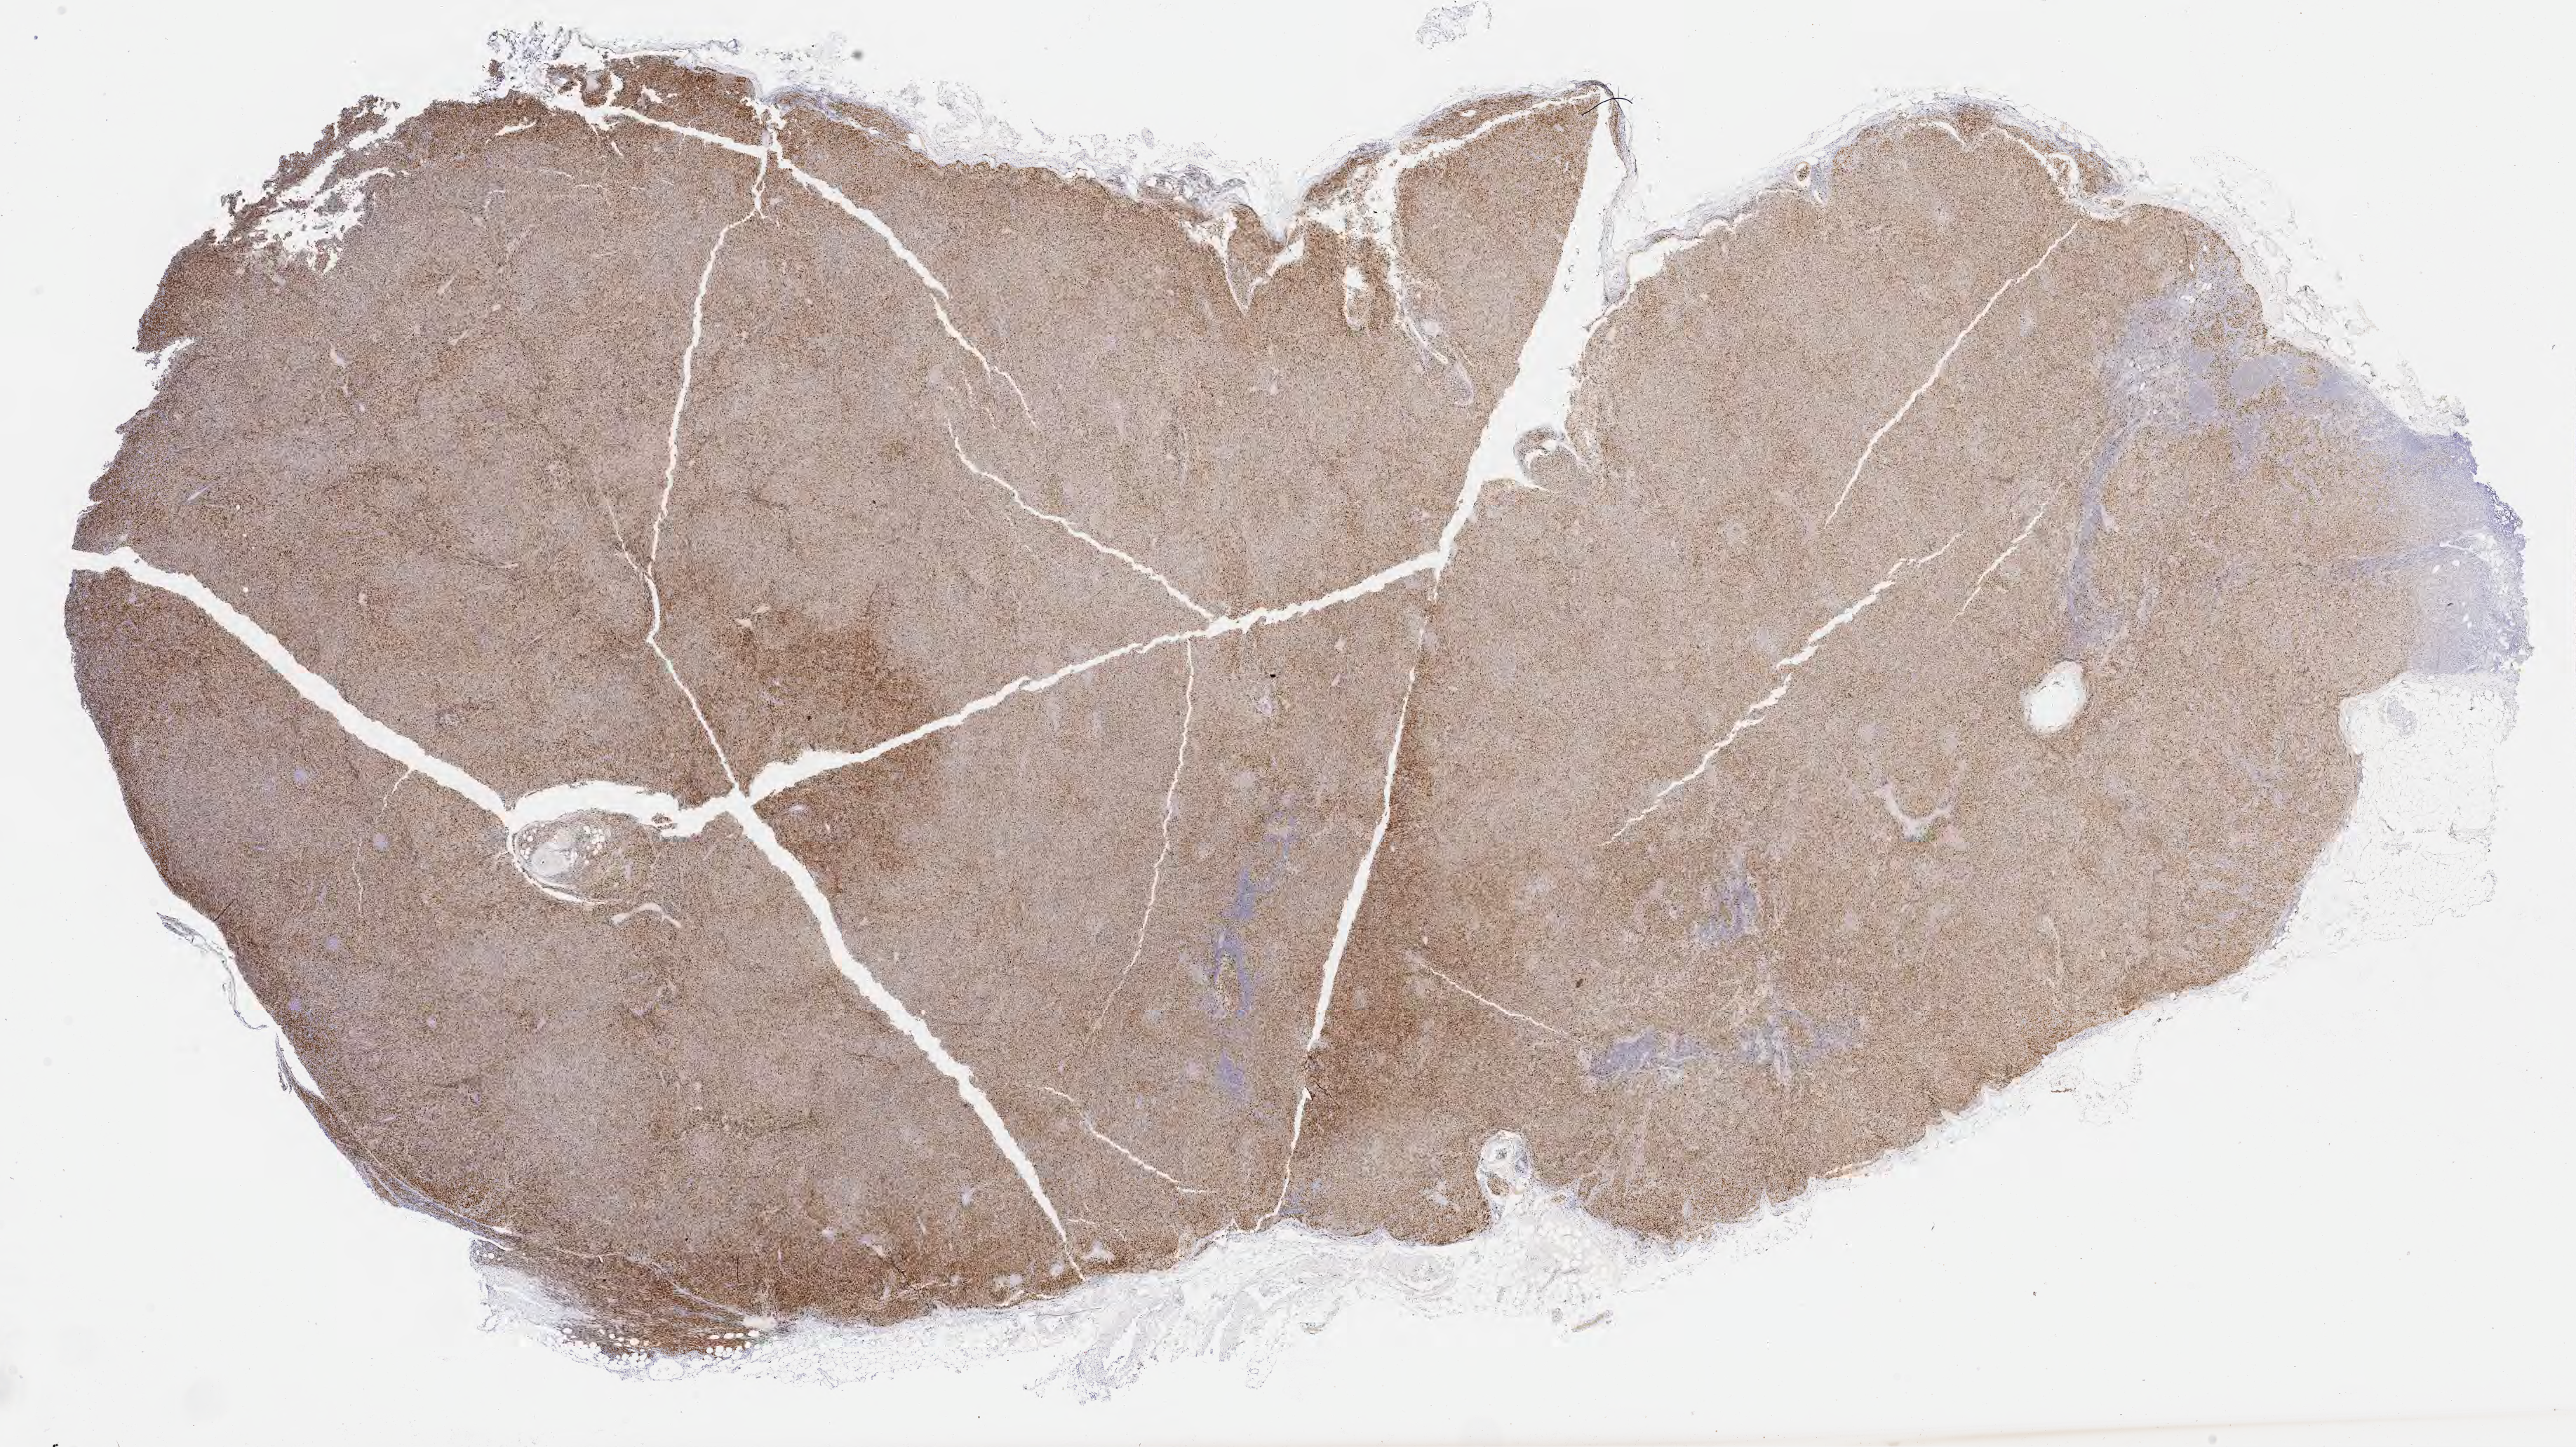
Whole-slide image, immunohistochemical stain for IRF4/MUM1, low-resolution overview of the scanned area, about 29.7 x 16.7 mm; specimen: tumor tissue. Male patient, age 69 years.
Diagnosis: Diffuse large B-cell lymphoma, NOS.